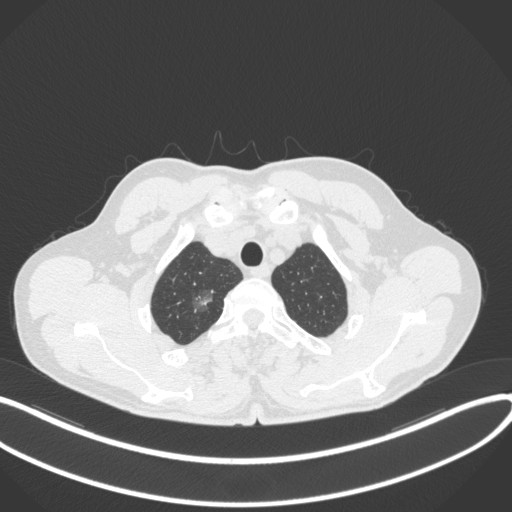
Chest CT, one axial slice. Slice 339 of 407 in the series (ordered by position). Lung window (W 1500 / L -600 HU). 512 × 512 image matrix, field of view 400 × 400 mm. Male patient, age 58 years. From the clinical record (not read from this slice): clinical TNM (as recorded): T1c N0 M0.
Annotated regions visible in this slice (rectangle marked by the reading radiologist):
- lung tumour (recorded histology: adenocarcinoma): bounding box (x1, y1, x2, y2) in pixels: (185, 286, 217, 318)